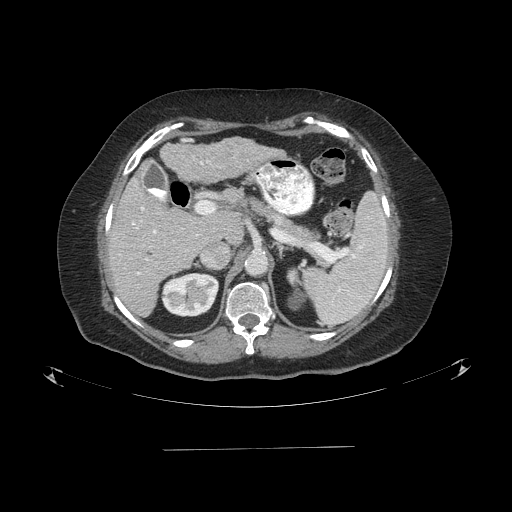
Contrast-enhanced abdominal CT (liver protocol), one axial slice; position 49 of 103 along the scan axis; one of 2 acquisitions stored at this slice position; soft-tissue window (W 400 / L 40 HU); 512 × 512 image matrix, field of view 500 × 500 mm. Case-level facts recorded for this patient, not image findings: diagnosis: hepatocellular carcinoma (patient treated with transarterial chemoembolisation; whether this scan precedes or follows treatment is not stated here); TNM stage (as recorded): Stage-IIIA; Child-Pugh class: A; tumour differentiation: poorly differentiated; tumour nodularity: multinodular.
Structures marked on this image (semi-automatically segmented with operator editing):
- liver parenchyma outside the tumour (the mass and vessels are separate outlines, so this box may not span the whole liver): bounding box [x1, y1, x2, y2] px = [106, 136, 280, 316]
- liver vessels: [133, 161, 209, 275]